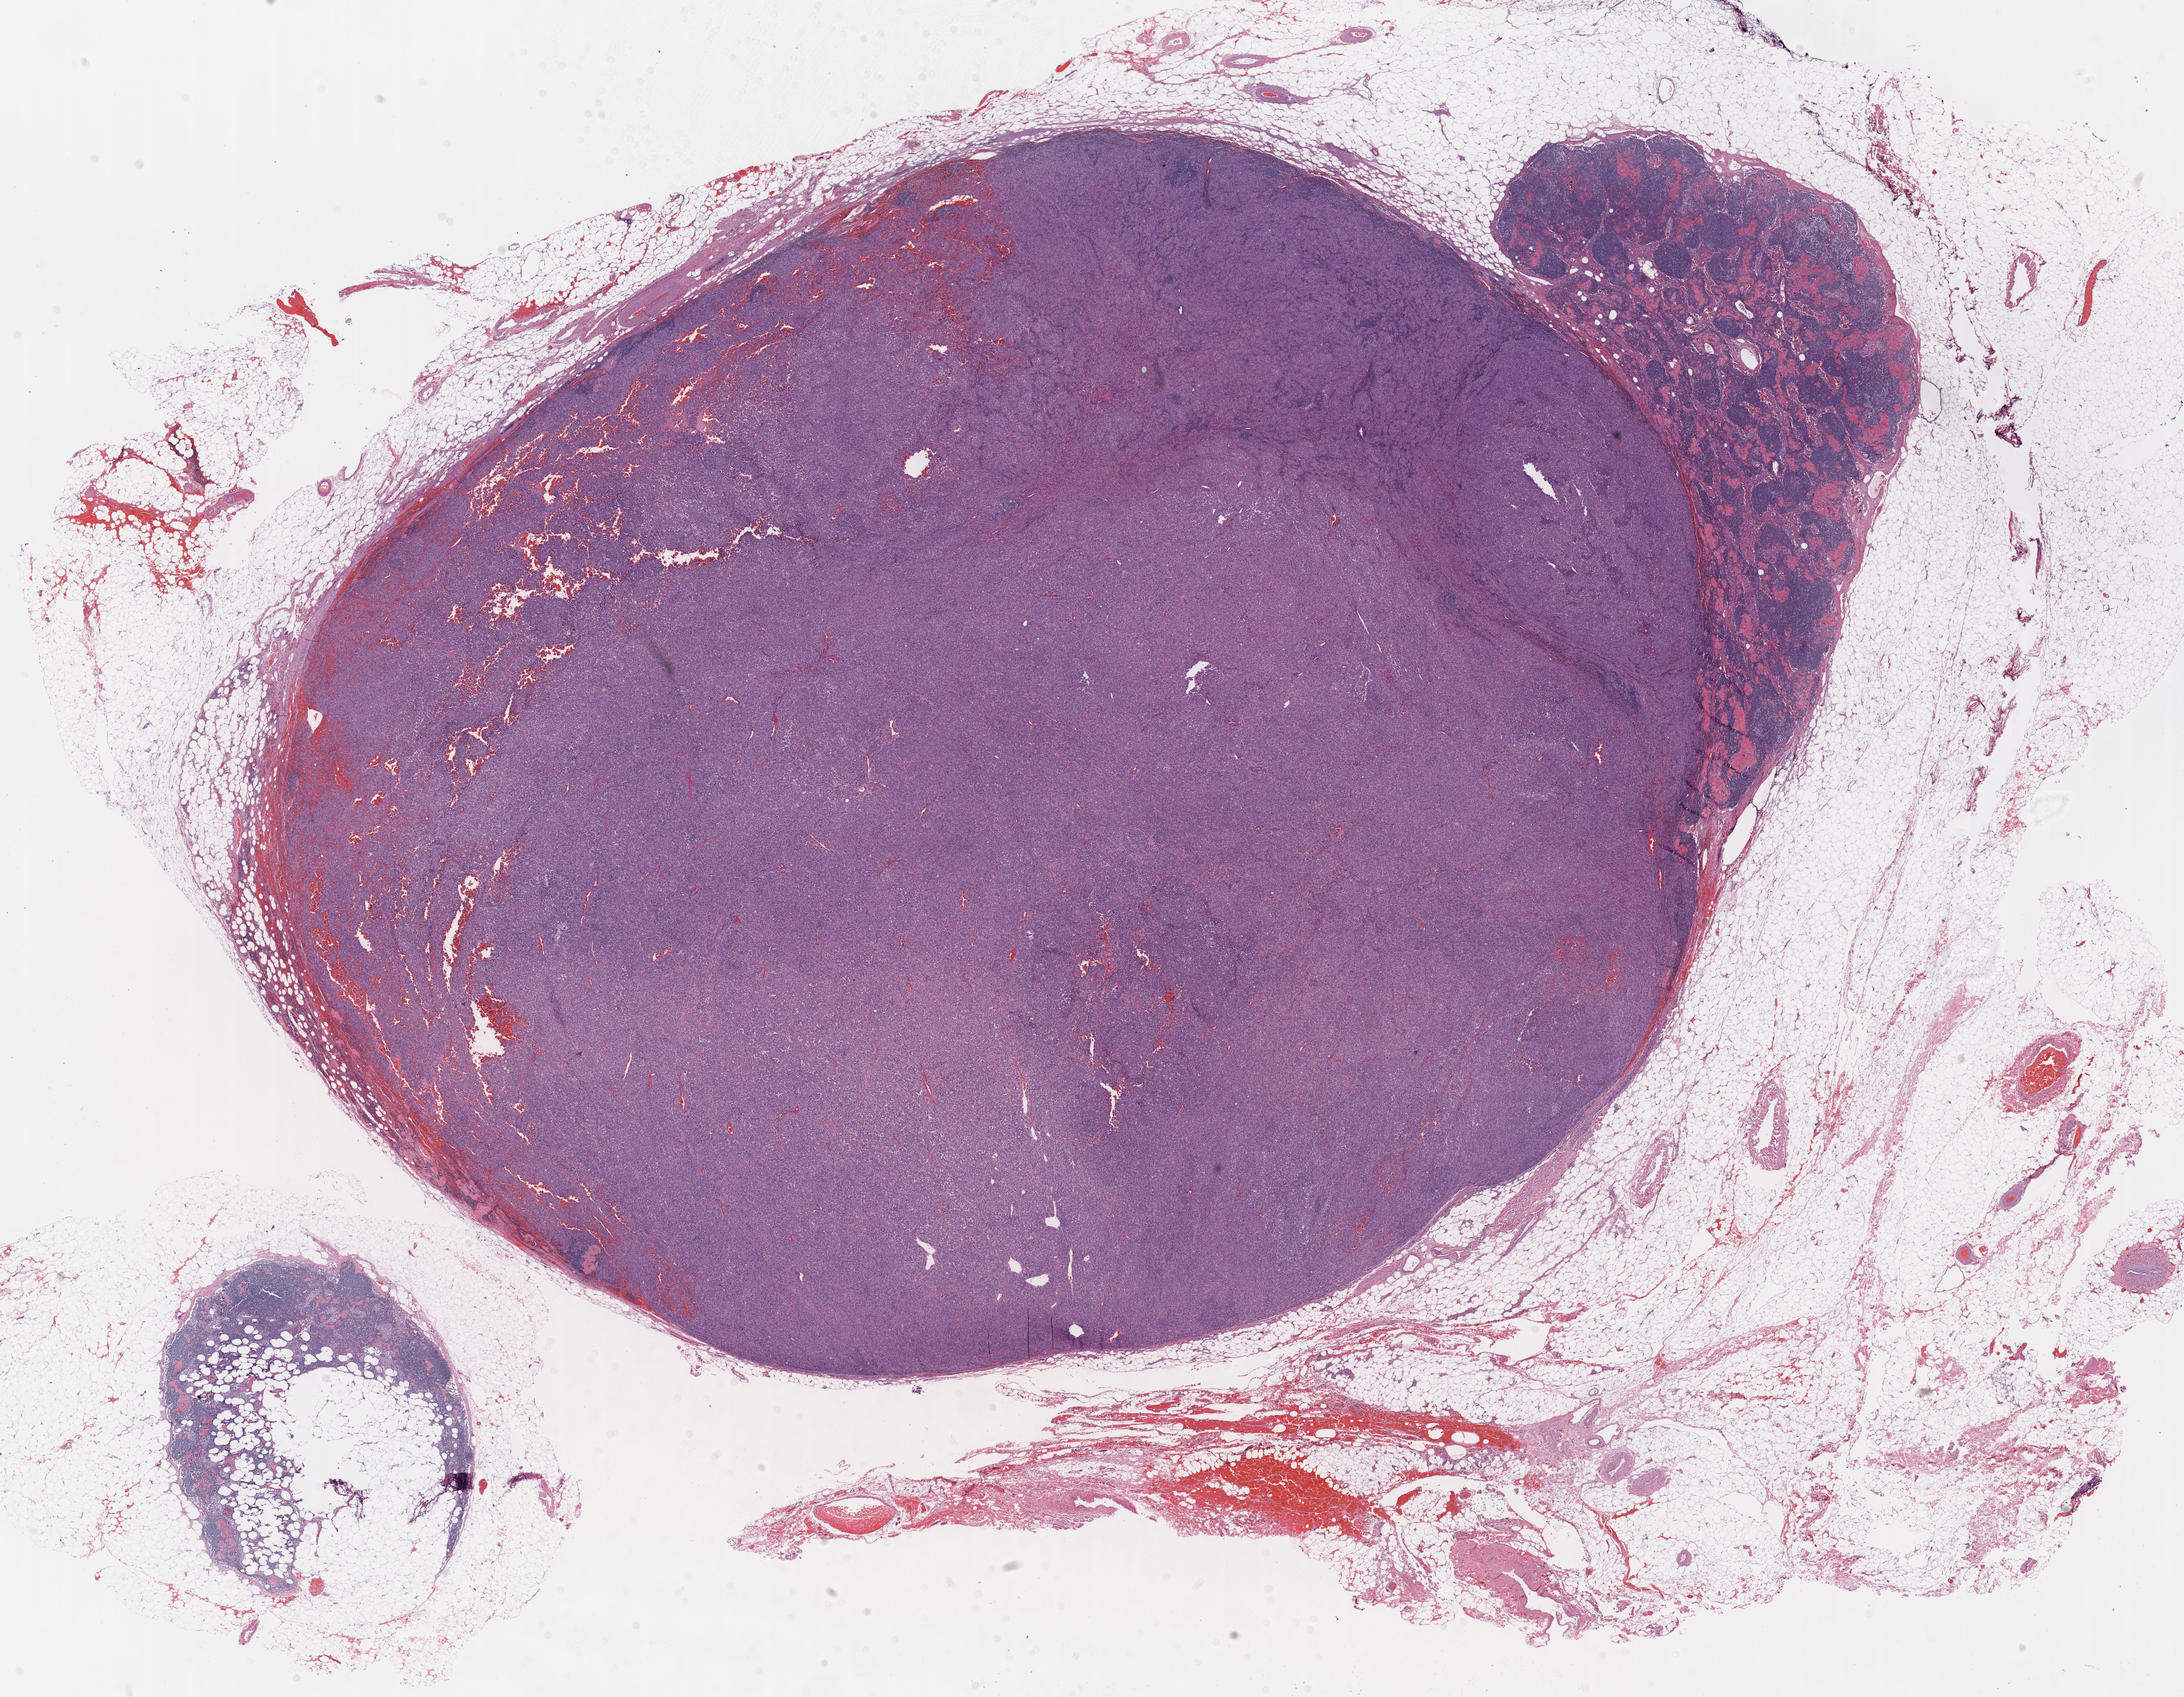
Digitized Hematoxylin and eosin (H&E) stained tissue section (whole slide) — whole scanned area (about 26.7 x 20.7 mm) shown as a low-resolution overview; FFPE section; metastatic tumour sample. Female patient; age at initial diagnosis 59 years.
This section: metastatic tumour tissue. Patient diagnosis: Malignant melanoma, NOS.